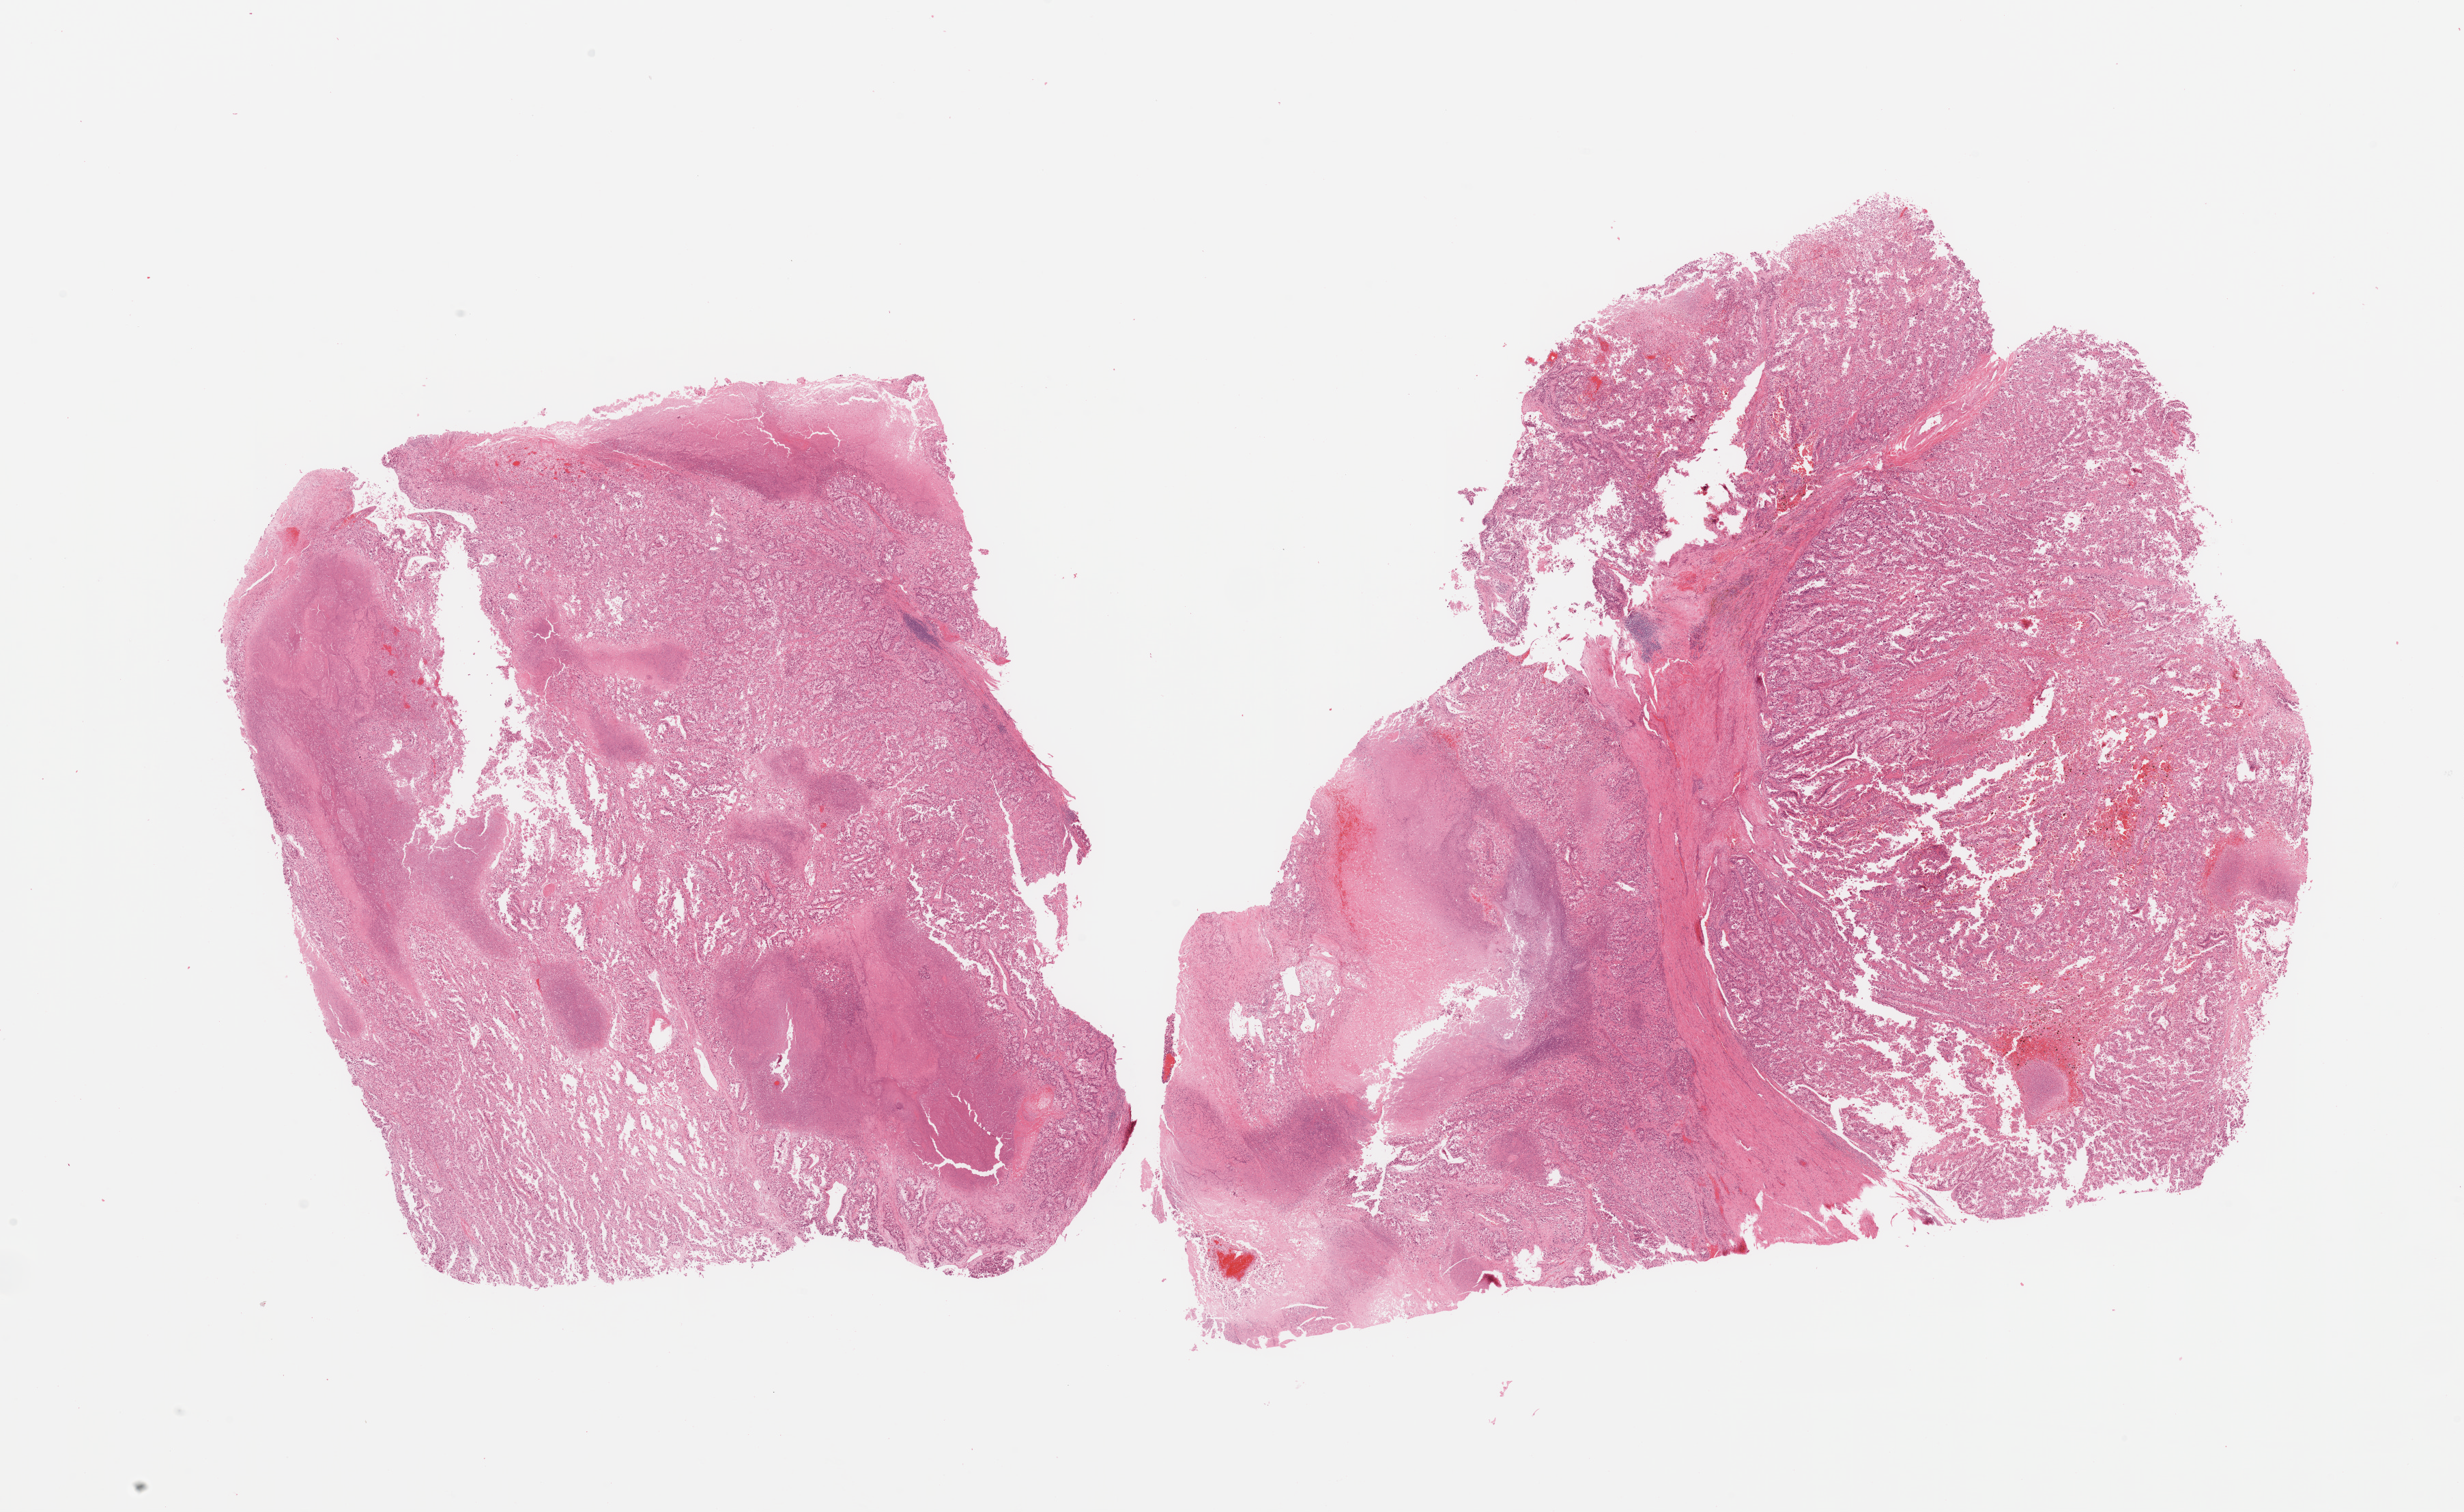
Hematoxylin and eosin (H&E) stained whole-slide image — low-resolution overview of the scanned area, about 28.5 x 17.5 mm. Tumour tissue sample, kidney. Female, 68 y/o.
Histologic diagnosis: Renal cell carcinoma, NOS.